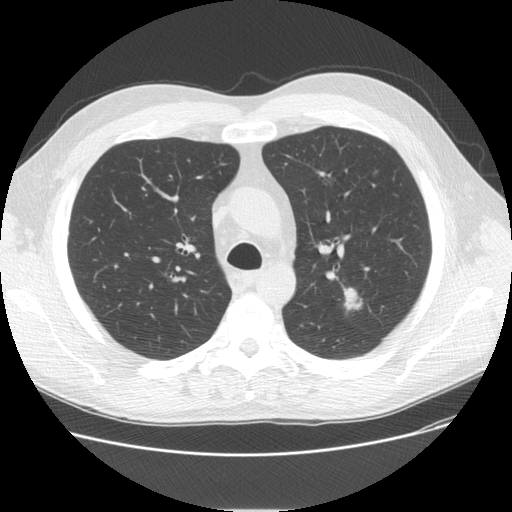
Low-dose screening chest CT, one axial slice. 120 kVp. Lung window (W 1500 / L -600 HU). 2.5 mm slice thickness. 512 × 512 image matrix, field of view 370 × 370 mm.
Structures marked on this image (expert manual segmentation):
- lesion 1 (tumor, upper lobe of left lung): bounding box (x1, y1, x2, y2) in pixels: (344, 288, 361, 310)